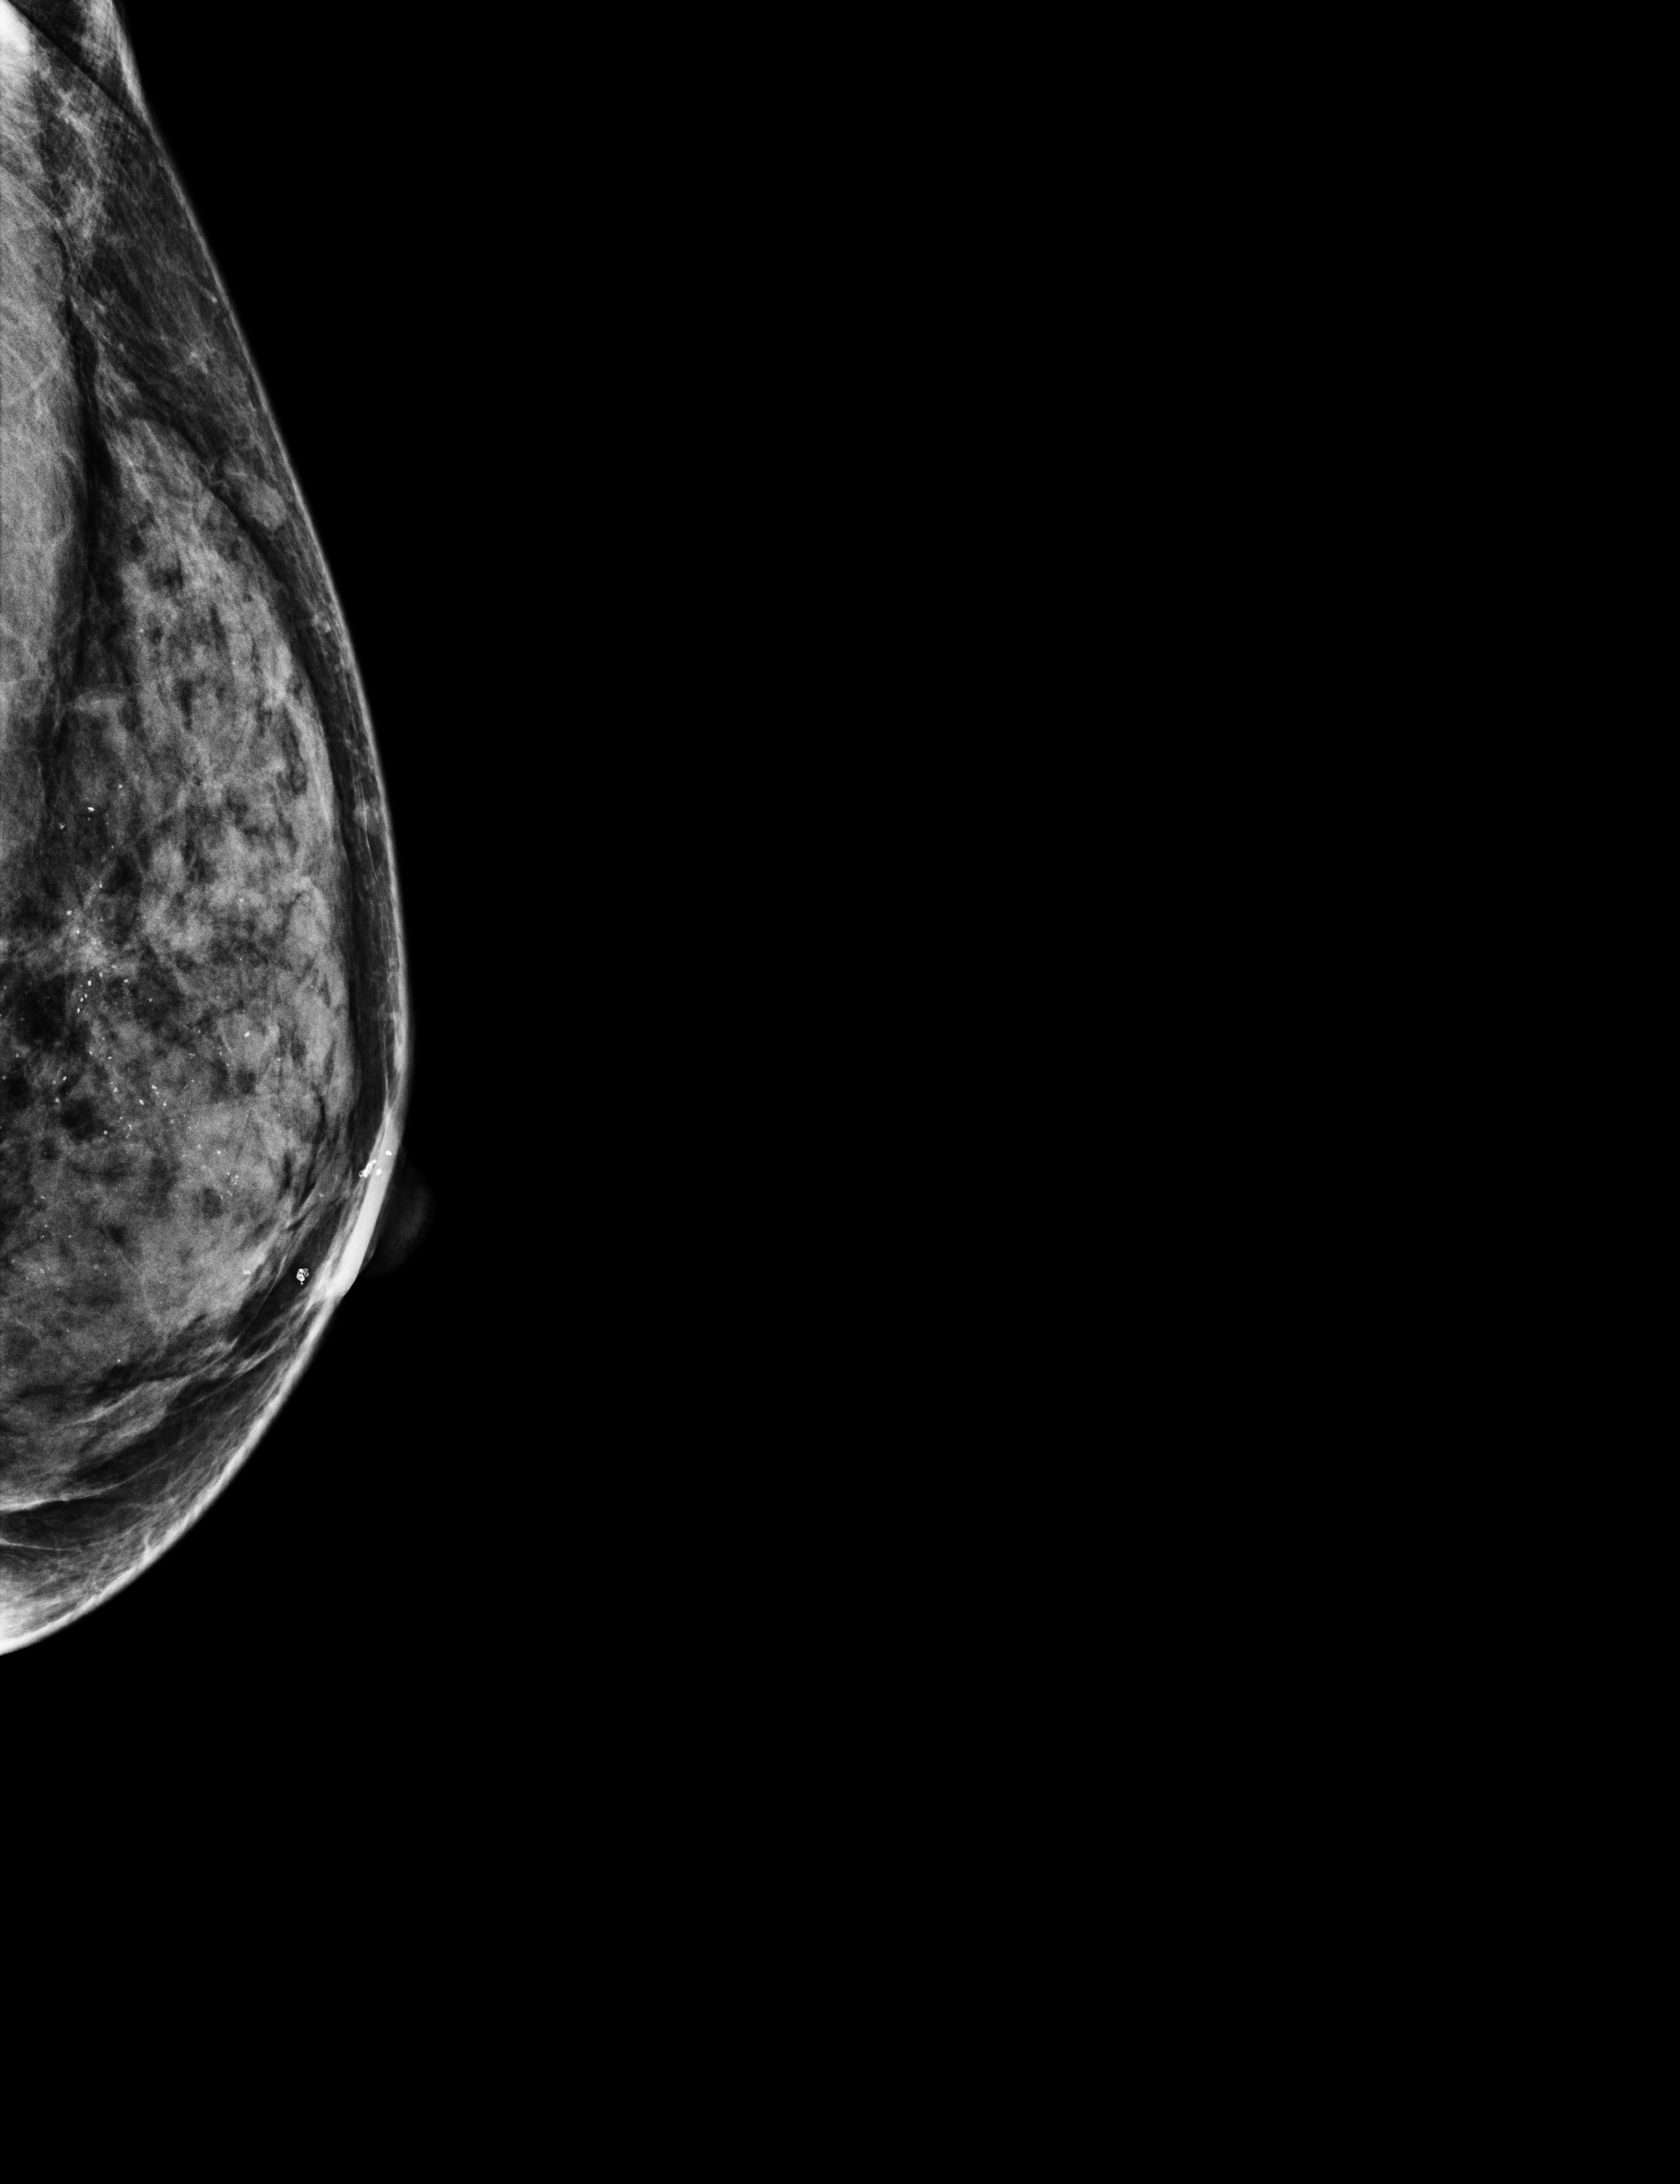
Annual screening mammography examination, compressed breast thickness 34 mm. Female patient, age 50 years.
Image type: full-field digital mammogram. Breast: left. Projection: exaggerated CC view (lateral).